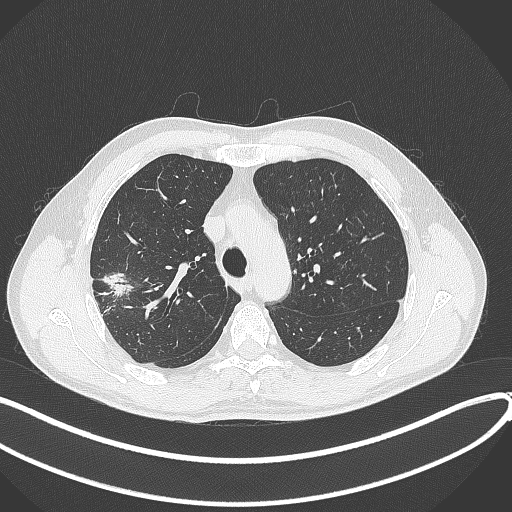
Chest CT, one axial slice; slice 307 of 381 in the series (ordered by position); 120 kVp; lung window (W 1500 / L -600 HU); 512 × 512 image matrix, field of view 400 × 400 mm. Patient: male, 62 years. From the clinical record (not read from this slice): clinical TNM (as recorded): T1c N0 M0; histopathological grade: G2-3.
Structures marked on this image (bounding box drawn by a radiologist):
- lung tumour (recorded histology: adenocarcinoma): box from (x=101, y=268) to (x=135, y=300) px